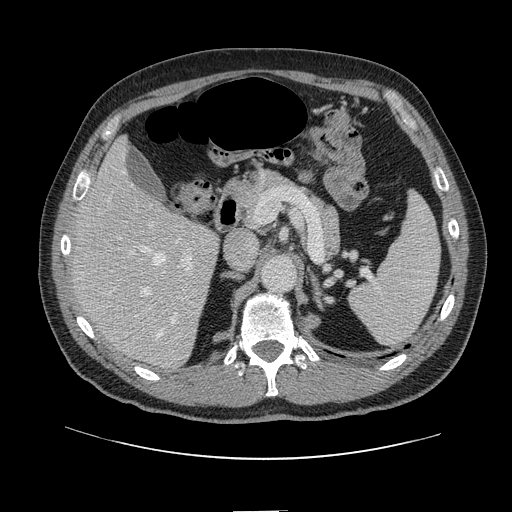
Contrast-enhanced abdominal CT, one axial slice. Position 77 of 161 along the scan axis. 120 kVp. Intravenous contrast given. Soft-tissue window (W 400 / L 40 HU). 512 × 512 image matrix, field of view 412 × 412 mm. Male patient, age 66 years. From the clinical record (not read from this slice): diagnosis: colorectal cancer liver metastases, imaged before liver resection; multiple liver metastases: no; largest metastasis: 3.5 cm; chemotherapy before resection: yes.
Structures marked on this image (expert manual segmentation):
- hepatic veins: bounding box [x1, y1, x2, y2] px = [122, 170, 177, 338]
- liver: [75, 141, 218, 368]
- planned liver remnant (the part of the liver to remain after resection): [75, 141, 200, 295]
- portal vein (with intrahepatic branches): [125, 221, 193, 314]